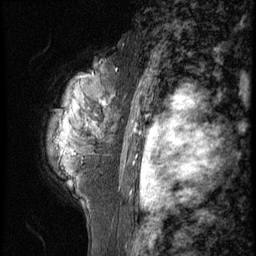
Breast MRI (dynamic contrast-enhanced), one sagittal slice. Position 41 of 56 along the scan axis. 3 images stored at this slice position (order not interpretable as contrast timing). 1.5 T. TE 4.2 ms, TR 9 ms. 2.5 mm slice thickness. 256 × 256 image matrix, field of view 180 × 180 mm. Female patient, age 50 years. From the clinical record (not read from this slice): setting: breast cancer imaged before/during neoadjuvant chemotherapy; receptor status: triple-negative.
Structures marked on this image (semi-automatic segmentation, software-assisted and operator-edited):
- analysis volume of interest (the breast-tissue region the enhancement analysis was run in; not a lesion): box from (x=43, y=54) to (x=127, y=191) px
- tumour enhancement mask (voxels above the 140 % enhancement threshold inside the analysis volume of interest): (x=103, y=101)–(x=106, y=106)